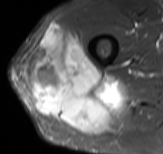
MRI of an extremity soft-tissue mass, one axial slice; slice 48 of 61 in the series (ordered by position); STIR; MR volume resampled by the dataset authors to the PET/CT grid (not the native acquisition matrix); 3.27 mm slice thickness; 163 × 154 image matrix, field of view 159 × 150 mm. Male patient. From the clinical record (not read from this slice): histological type: poorly differentiated synovial sarcoma; grade: high; site of the primary tumour: right buttock.
Outlined on this slice (expert contour drawn on MRI and transferred to this co-registered scan by the dataset authors):
- gross tumour volume including surrounding oedema: bounding box (x1, y1, x2, y2) in pixels: (27, 25, 122, 129)
- gross tumour volume (mass): (27, 25, 122, 129)